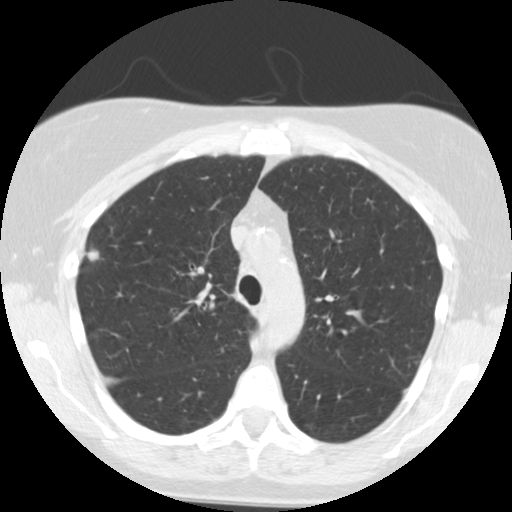
Axial slice from a low-dose chest CT screening exam; second screening round (one year after baseline); lung window (W 1500 / L -600 HU); 2.5 mm slice thickness; standard (soft-tissue) reconstruction kernel (STANDARD); slice 171 of 244 in the series; 512 × 512 image matrix, field of view 312 × 312 mm. Female participant, aged 55 years at enrolment.
- Expert-annotated lung lesion, bounding box [x1, y1, x2, y2] px = [69, 238, 115, 275].
- No non-calcified nodule or mass ≥4 mm was recorded by the screening reader at this exam.
- Official screen result: negative screen, minor abnormalities not suspicious for lung cancer.
- Participant outcome: lung cancer diagnosed 621 days after this screen — bronchiolo-alveolar adenocarcinoma, NOS, right upper lobe, moderately differentiated (G2), stage IIA (AJCC 6th edition), 13 mm at pathology.